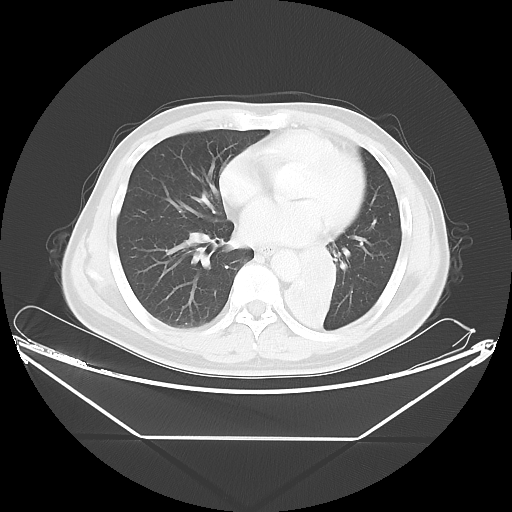
Chest CT, one axial slice; position 20 of 48 along the scan axis; 120 kVp; lung window (W 1500 / L -600 HU); 5 mm slice thickness; 512 × 512 image matrix, field of view 438 × 438 mm. Male patient, age 58 years. Case-level facts recorded for this patient, not image findings: clinical TNM (as recorded): T3 N3 M0.
Outlined on this slice (rectangle marked by the reading radiologist):
- lung tumour (recorded histology: squamous cell carcinoma): bounding box [x1, y1, x2, y2] px = [276, 243, 358, 336]